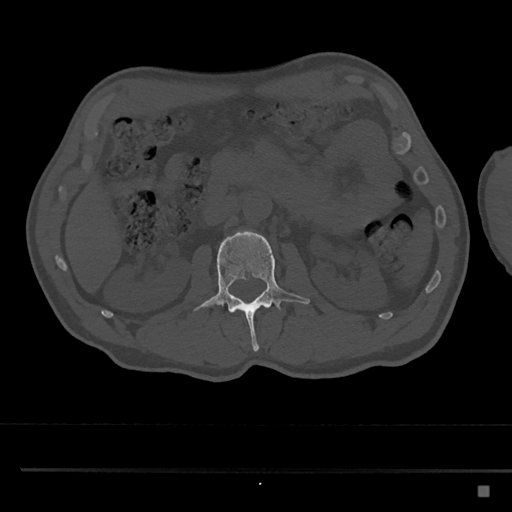
CT including the spine, one axial slice. Slice 762 of 797 in the series (ordered by position). Bone window (W 1800 / L 400 HU). 512 × 512 image matrix, field of view 391 × 391 mm. Male patient, age 59 years. From the clinical record (not read from this slice): primary cancer: prostate.
Structures marked on this image (semi-automatic segmentation, software-assisted and operator-edited):
- L2 vertebra: bounding box (x1, y1, x2, y2) in pixels: (194, 230, 310, 352)